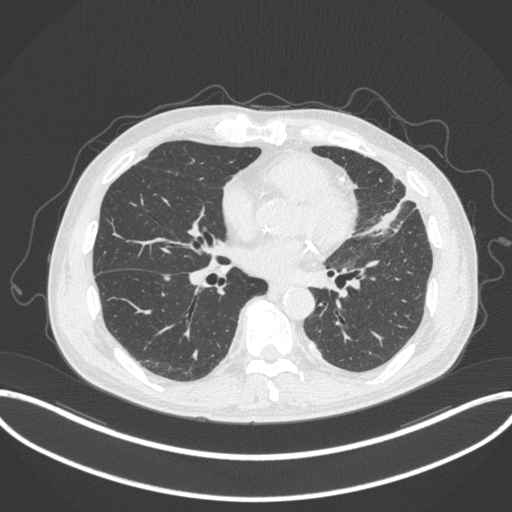
Chest CT, one axial slice; position 146 of 382 along the scan axis; reconstruction kernel B31f; lung window (W 1500 / L -600 HU); 512 × 512 image matrix, field of view 415 × 415 mm. Patient: male, 64 years. Case-level facts recorded for this patient, not image findings: clinical TNM (as recorded): T4 N1 M0; histopathological grade: G3.
Outlined on this slice (bounding box drawn by a radiologist):
- lung tumour (recorded histology: adenocarcinoma): bounding box (x1, y1, x2, y2) in pixels: (361, 189, 420, 240)